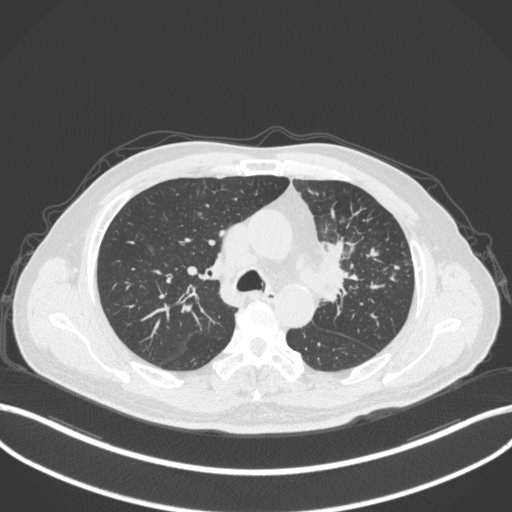
Chest CT, one axial slice; position 232 of 386 along the scan axis; 120 kVp; lung window (W 1500 / L -600 HU); 1 mm slice thickness; 512 × 512 image matrix. Male patient, age 69 years. Case-level facts recorded for this patient, not image findings: clinical TNM (as recorded): T2a N2 M0.
Outlined on this slice (rectangle marked by the reading radiologist):
- lung tumour (recorded histology: adenocarcinoma): bounding box <317,230,355,307> (left, top, right, bottom; pixels)